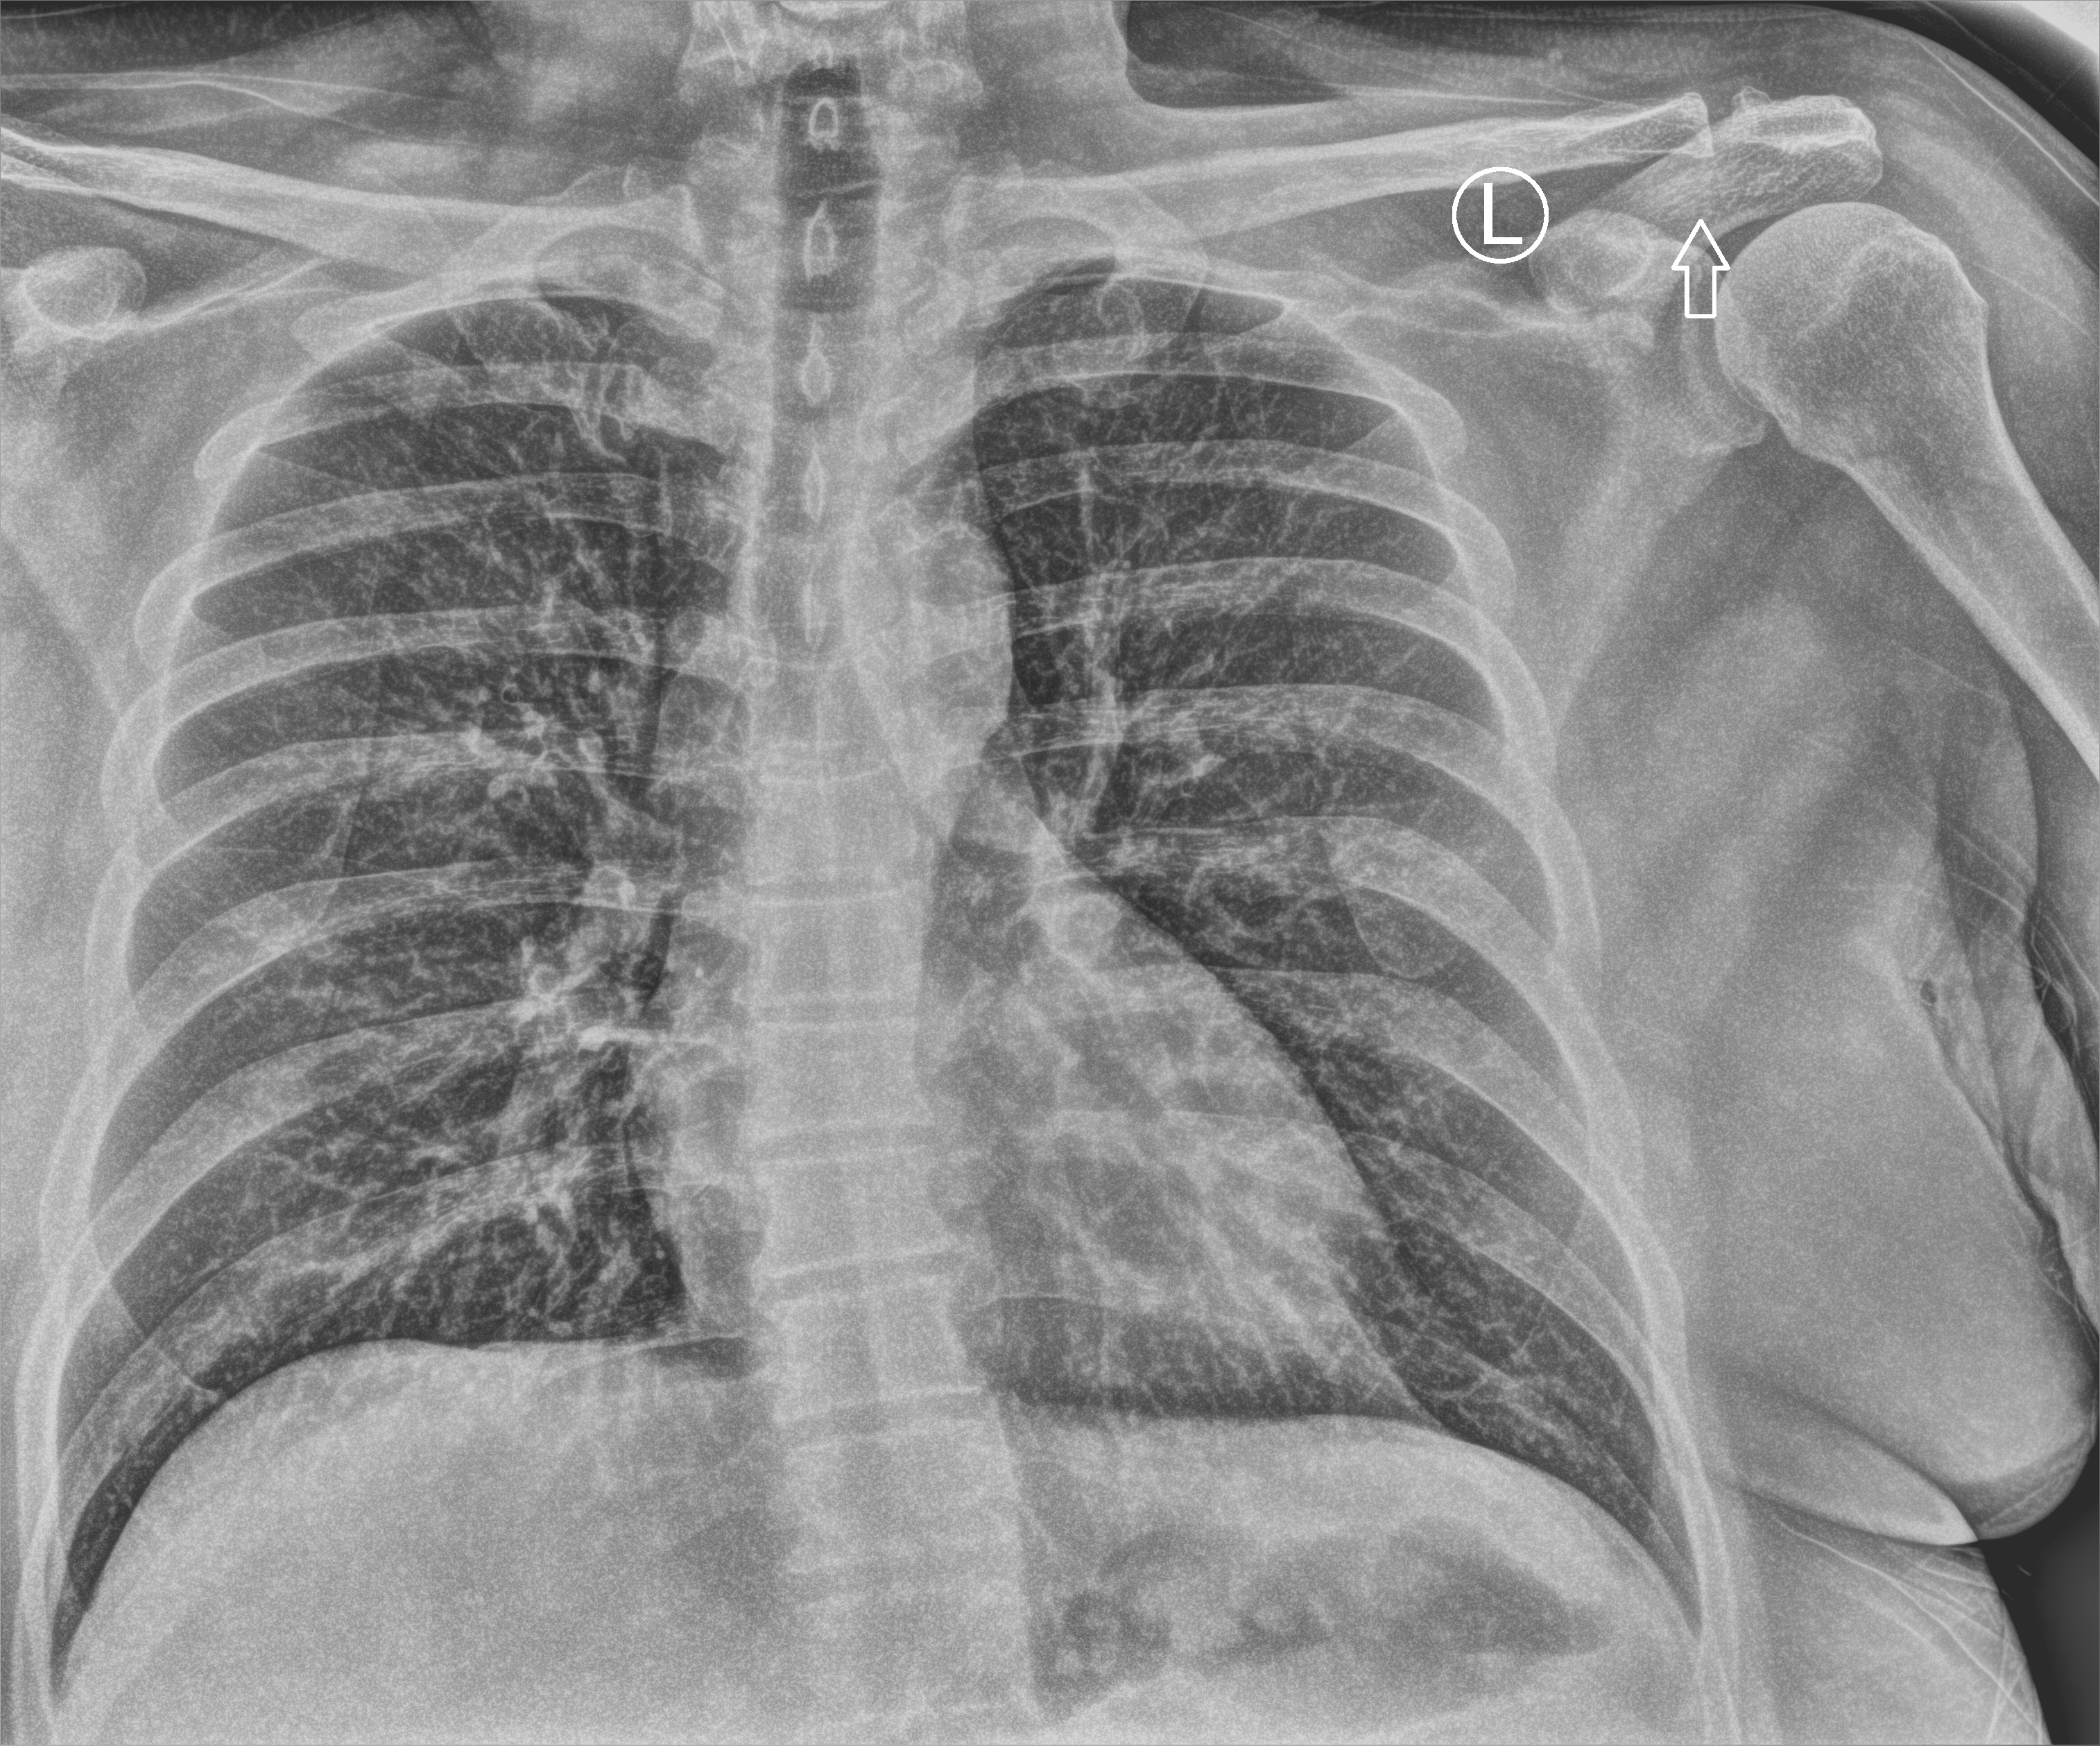
Chest X-ray (portable). Male patient hospitalised with COVID-19, age 60–74 years.
Hospital-stay facts (about this admission, not read from this image; timing relative to this image not recorded): COPD (admission record): no; mechanically ventilated during this hospital stay: no; admitted to intensive care during this hospital stay: no.